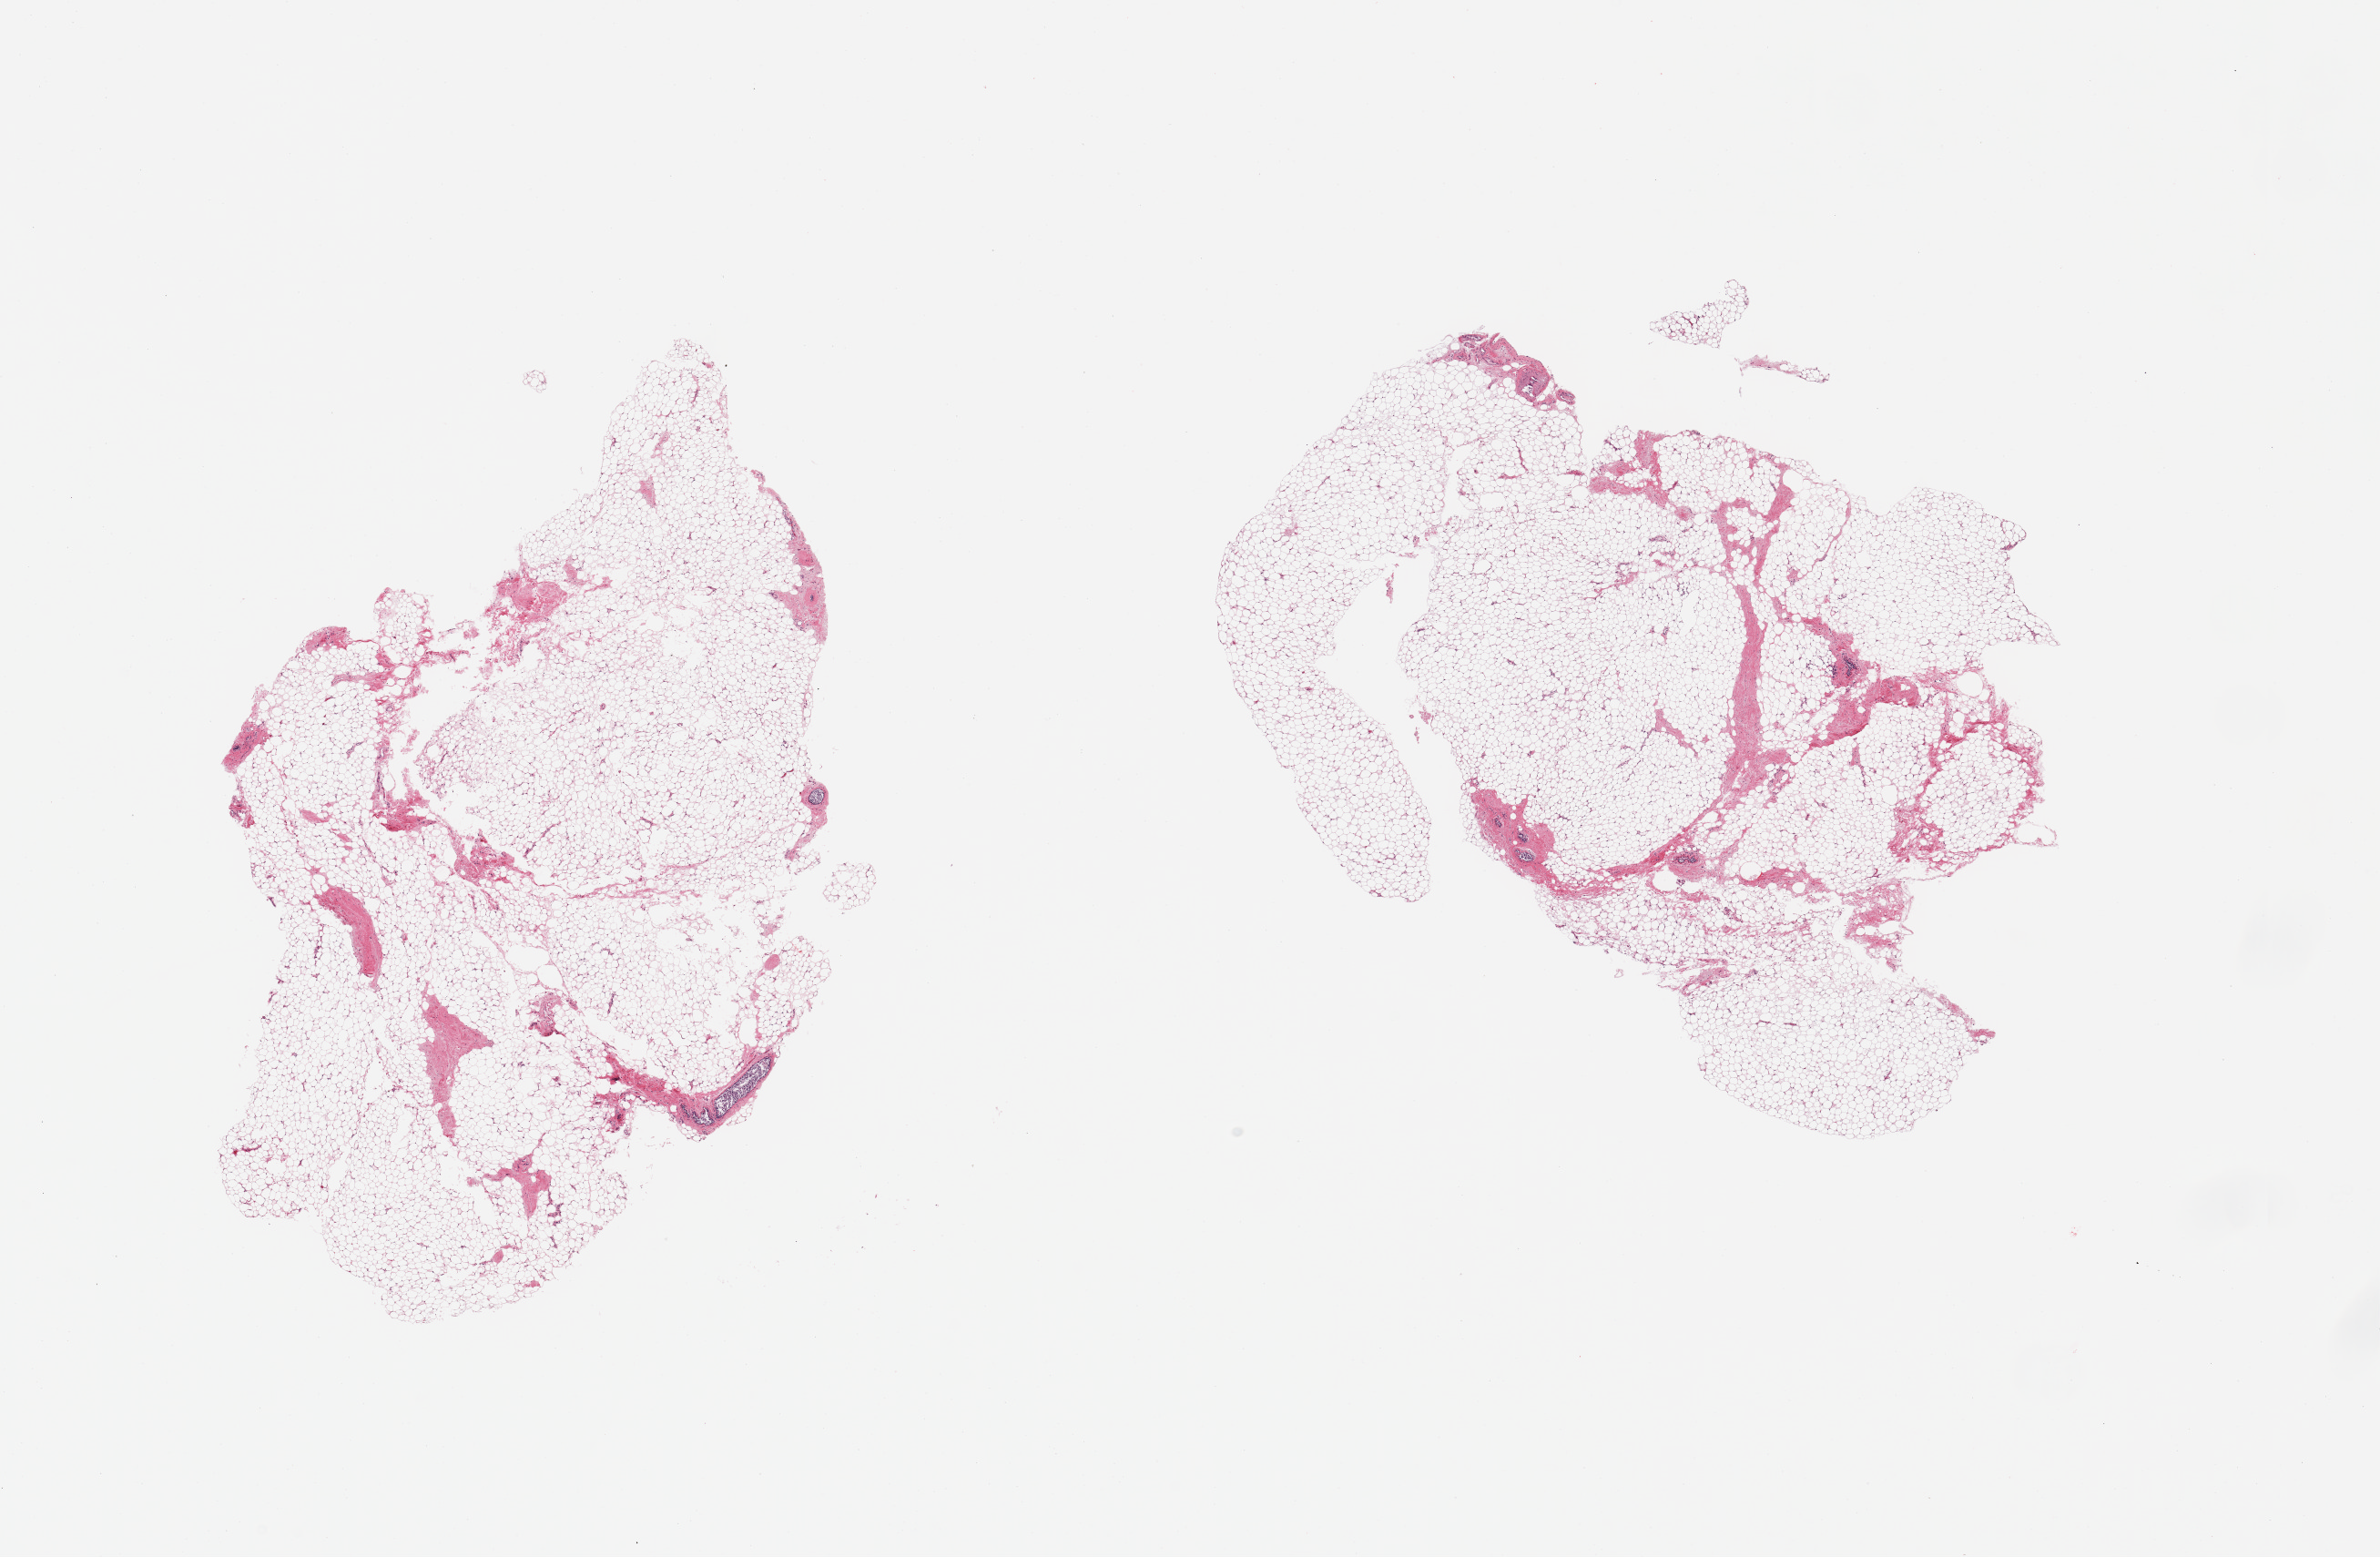
Whole-slide image, haematoxylin and eosin stain, brightfield, a low-resolution overview of the entire scanned area, about 20.7 x 13.5 mm; PAXgene-fixed paraffin-embedded (PFPE) section; target tissue: breast; donor tissue sample. Donor: female.
- pathologist's review note for this sample: 2 pieces, fibroadipose elements, trace atrophic ductal structures